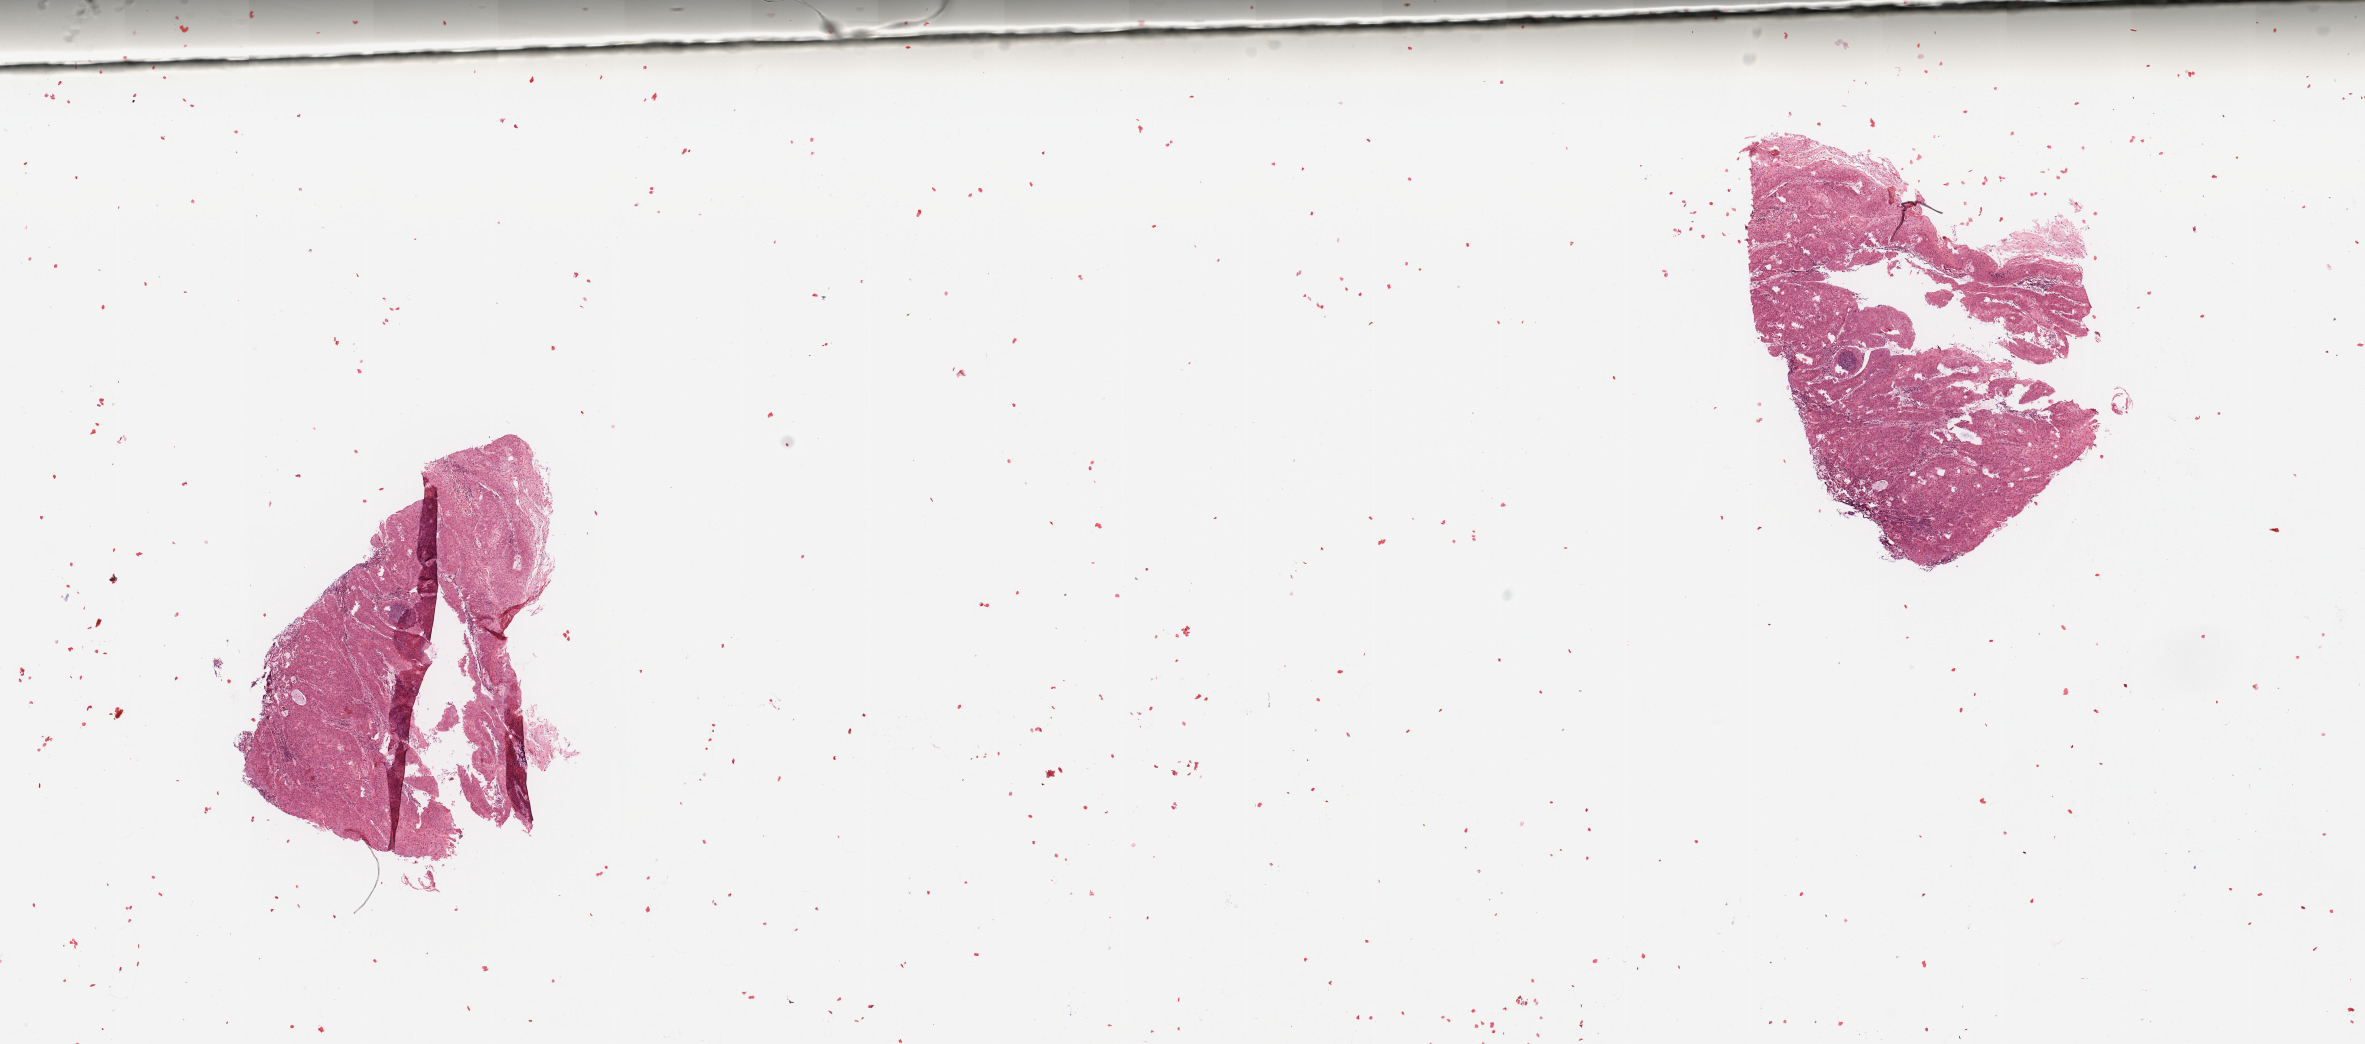
Whole-slide histology image, H&E, shown as a low-resolution overview of the whole scanned area (about 18.7 x 8.3 mm, acquisition: 20x scan), tumour tissue sample, sampled site: larynx. 69-year-old male patient. Histologic grade: G2 (moderately differentiated). Composition of this section per pathologist review: tumour nuclei 90%, necrosis 5%.
Histologic diagnosis: Squamous cell carcinoma, NOS (larynx, NOS). AJCC pathologic stage: IVA.